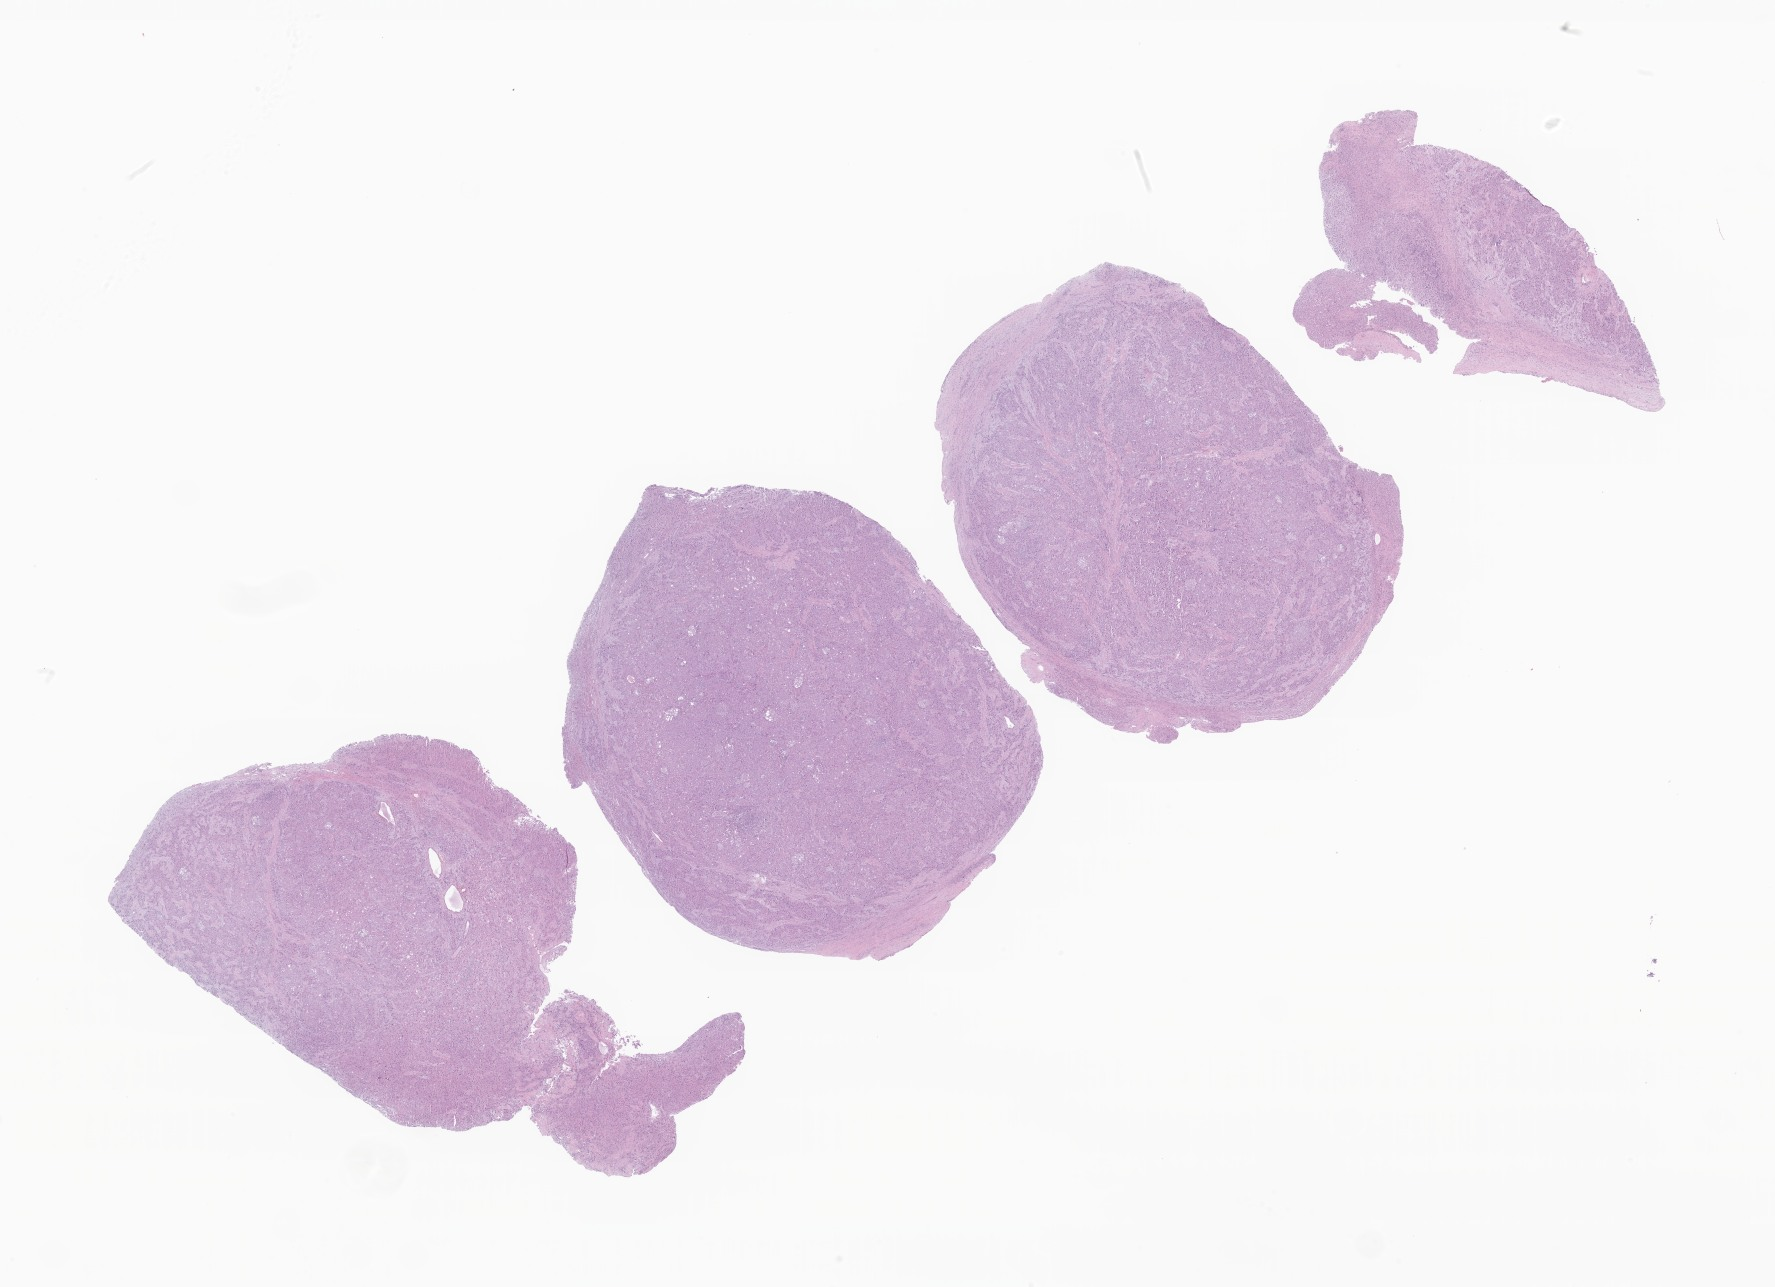
Whole-slide image, H&E stain of tumor tissue from the liver, whole scanned area (about 29.9 x 21.7 mm) shown as a low-resolution overview, FFPE section. Female patient, age 179 months (14 years 11 months).
* diagnosis (ICD-O-3 morphology term): Hepatocellular carcinoma, fibrolamellar